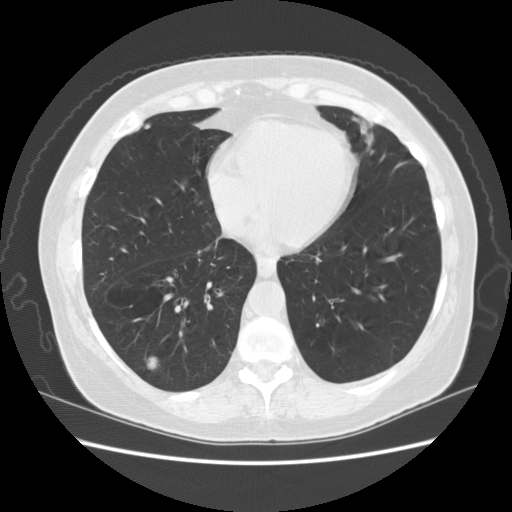
Low-dose screening chest CT, one axial slice. Position 48 of 156 along the scan axis. Reconstruction kernel STANDARD. 120 kVp. Lung window (W 1500 / L -600 HU). 512 × 512 image matrix, field of view 360 × 360 mm.
Structures marked on this image (manually delineated by an expert):
- lesion 1 (tumor, lower lobe of right lung): bounding box (x1, y1, x2, y2) in pixels: (148, 358, 156, 368)